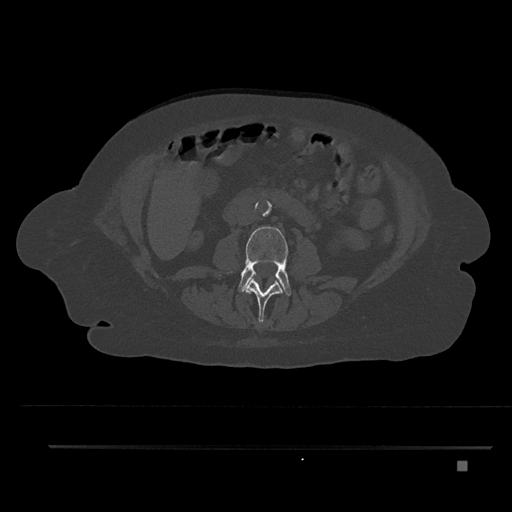
CT including the spine, one axial slice; slice 148 of 797 in the series (ordered by position); bone window (W 1800 / L 400 HU); 0.5 mm slice thickness; 512 × 512 image matrix, field of view 437 × 437 mm. Female patient, age 76 years. Case-level facts recorded for this patient, not image findings: primary cancer: lung.
Structures marked on this image (semi-automatic segmentation, software-assisted and operator-edited):
- L2 vertebra: bounding box (x1, y1, x2, y2) in pixels: (245, 279, 283, 323)
- L3 vertebra: (238, 226, 292, 296)